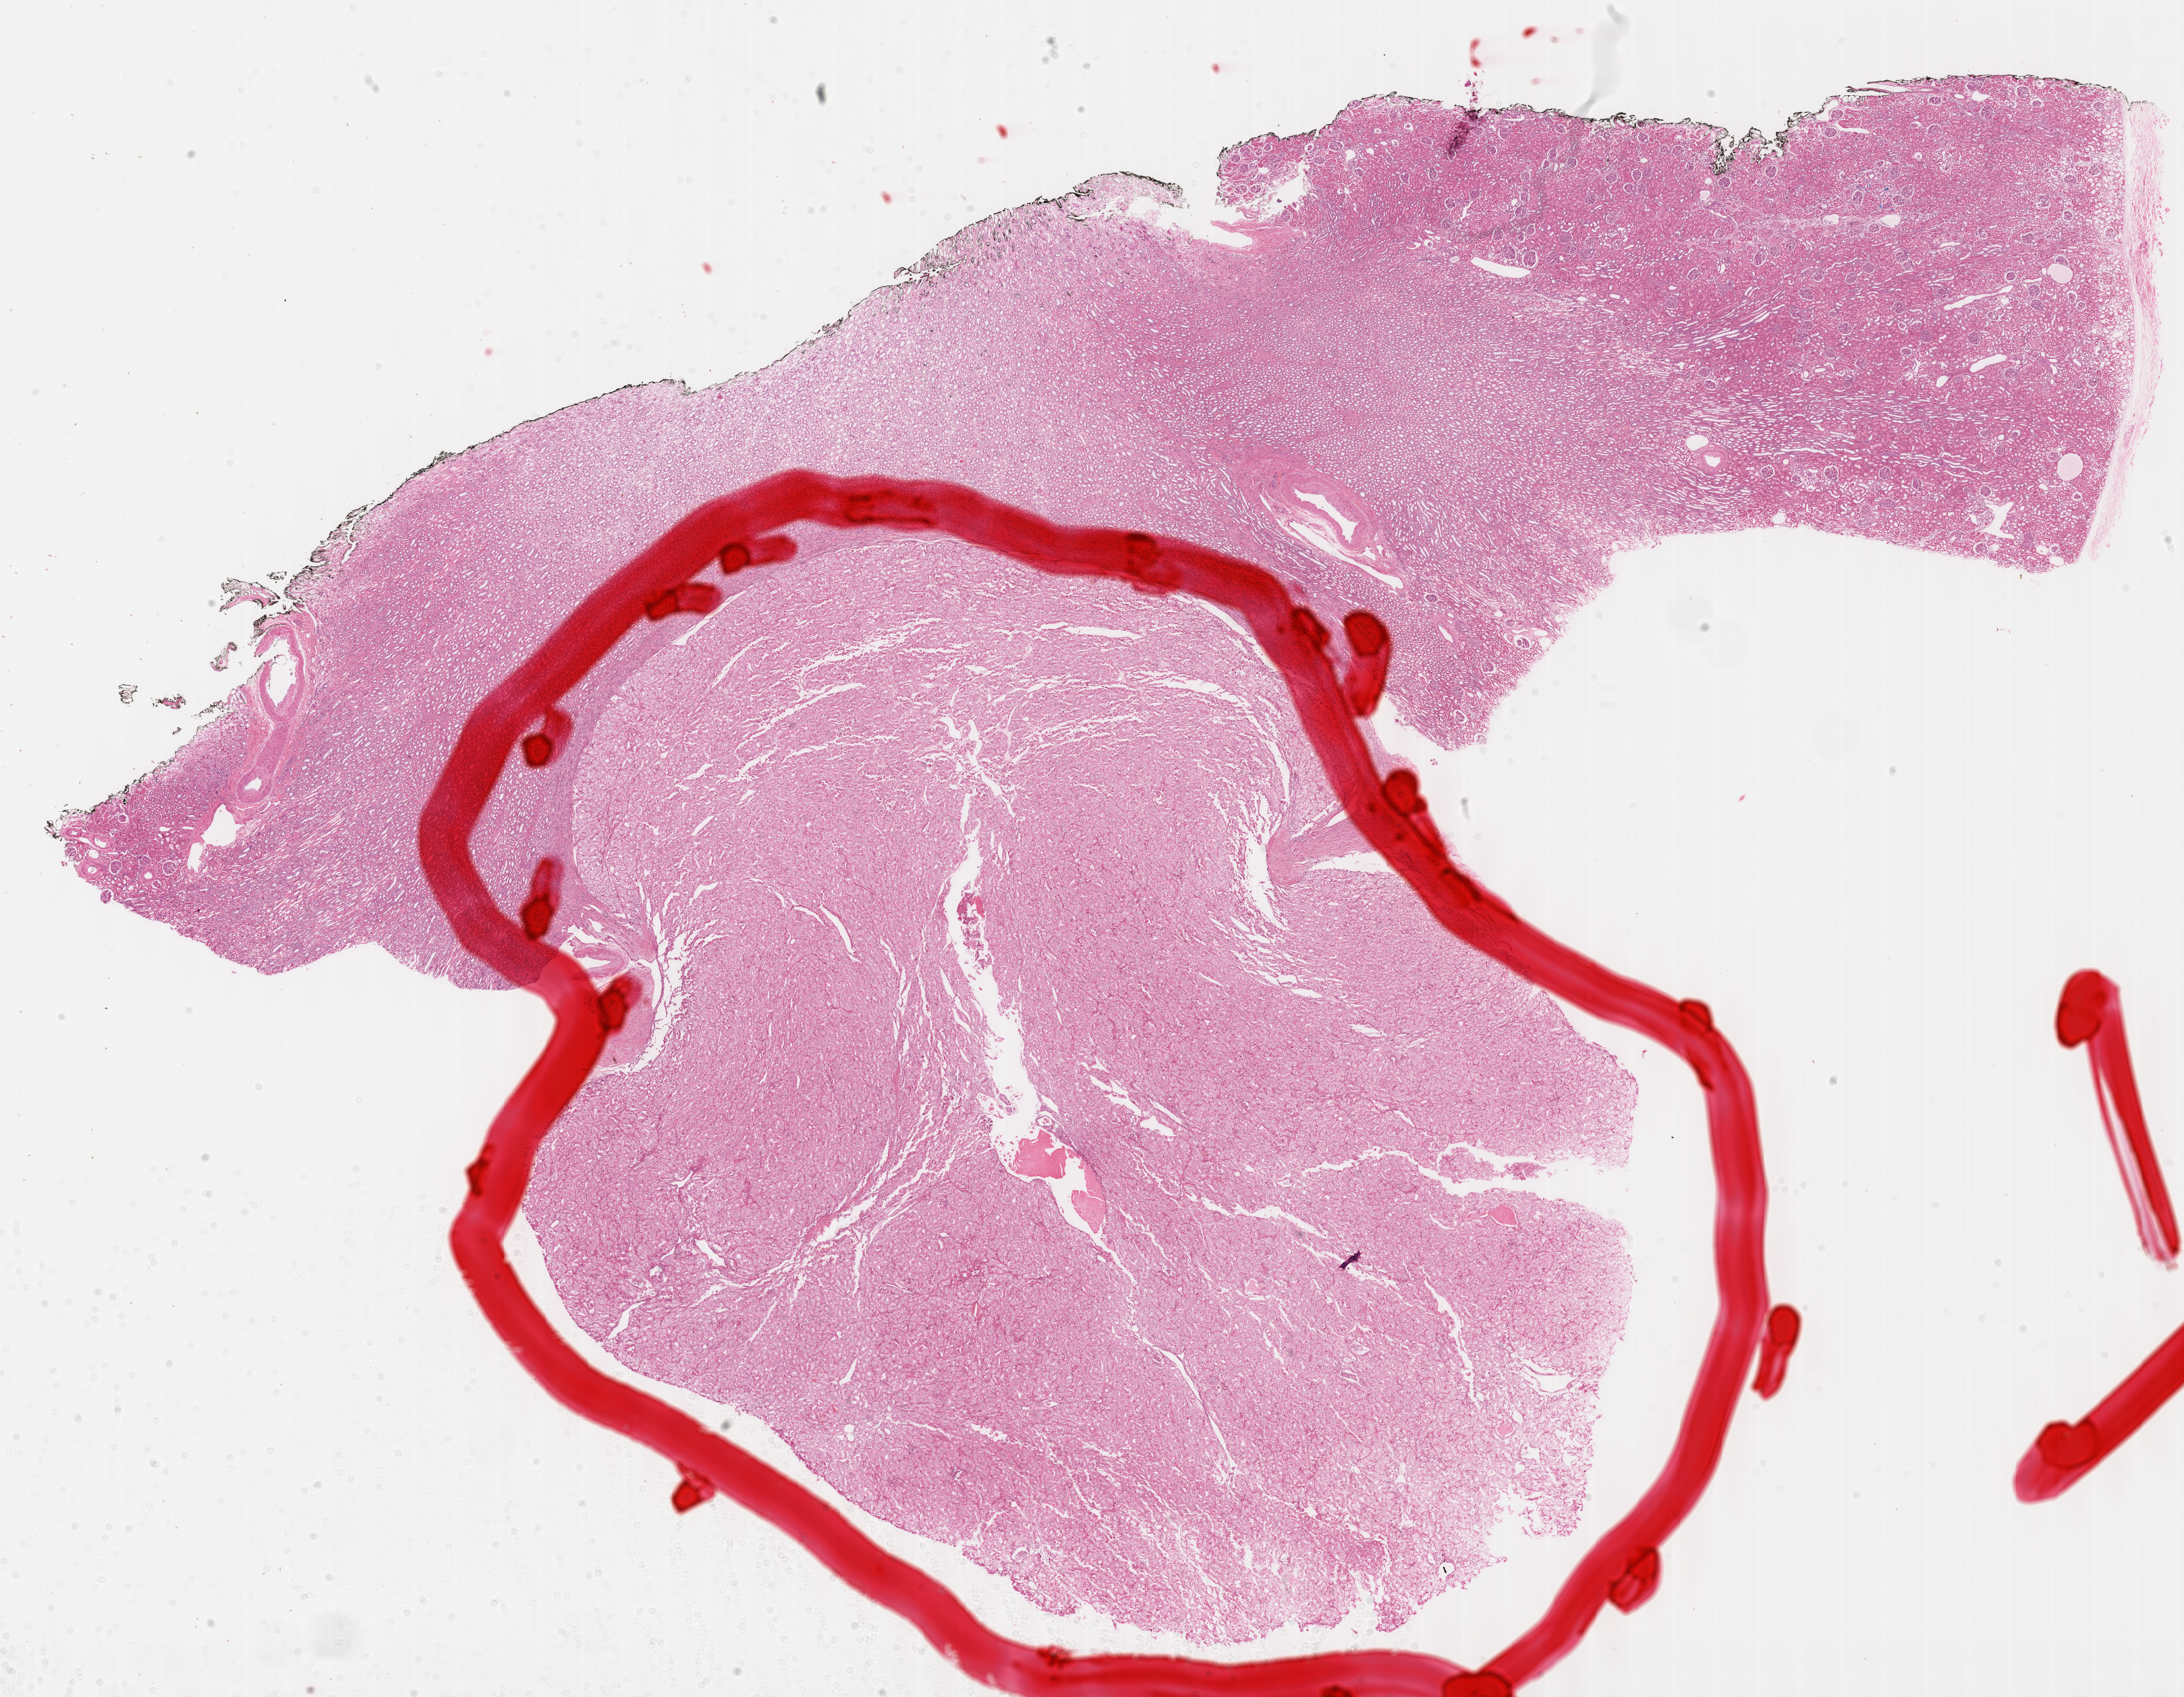
Whole-slide histology image, H&E, low-resolution overview of the scanned area, about 26.2 x 20.3 mm (from a 40x scan); FFPE section; primary tumour sample from the kidney. Female patient; age at initial diagnosis 36 years. Pathologist review of this section (percent, as recorded): tumour cells 92%, tumour nuclei 95%, normal cells 4%, stromal cells 4%, necrosis 0%. Infiltration values recorded for this section: lymphocyte infiltration 2%, monocyte infiltration 0%, neutrophil infiltration 0%.
Laterality: left. Pathologic diagnosis: Renal cell carcinoma, chromophobe type. AJCC pathologic stage: I (7th edition).